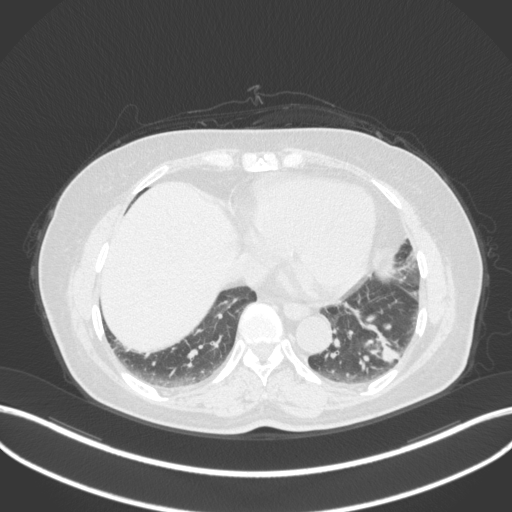
Chest CT, one axial slice; position 118 of 307 along the scan axis; reconstruction kernel B31f; 120 kVp; lung window (W 1500 / L -600 HU); 1 mm slice thickness; 512 × 512 image matrix, field of view 400 × 400 mm. Patient: female, 59 years. From the clinical record (not read from this slice): clinical TNM (as recorded): T2a N0 M0; histopathological grade: G2-3.
Annotated regions visible in this slice (bounding box drawn by a radiologist):
- lung tumour (recorded histology: adenocarcinoma): box from (x=361, y=321) to (x=408, y=373) px